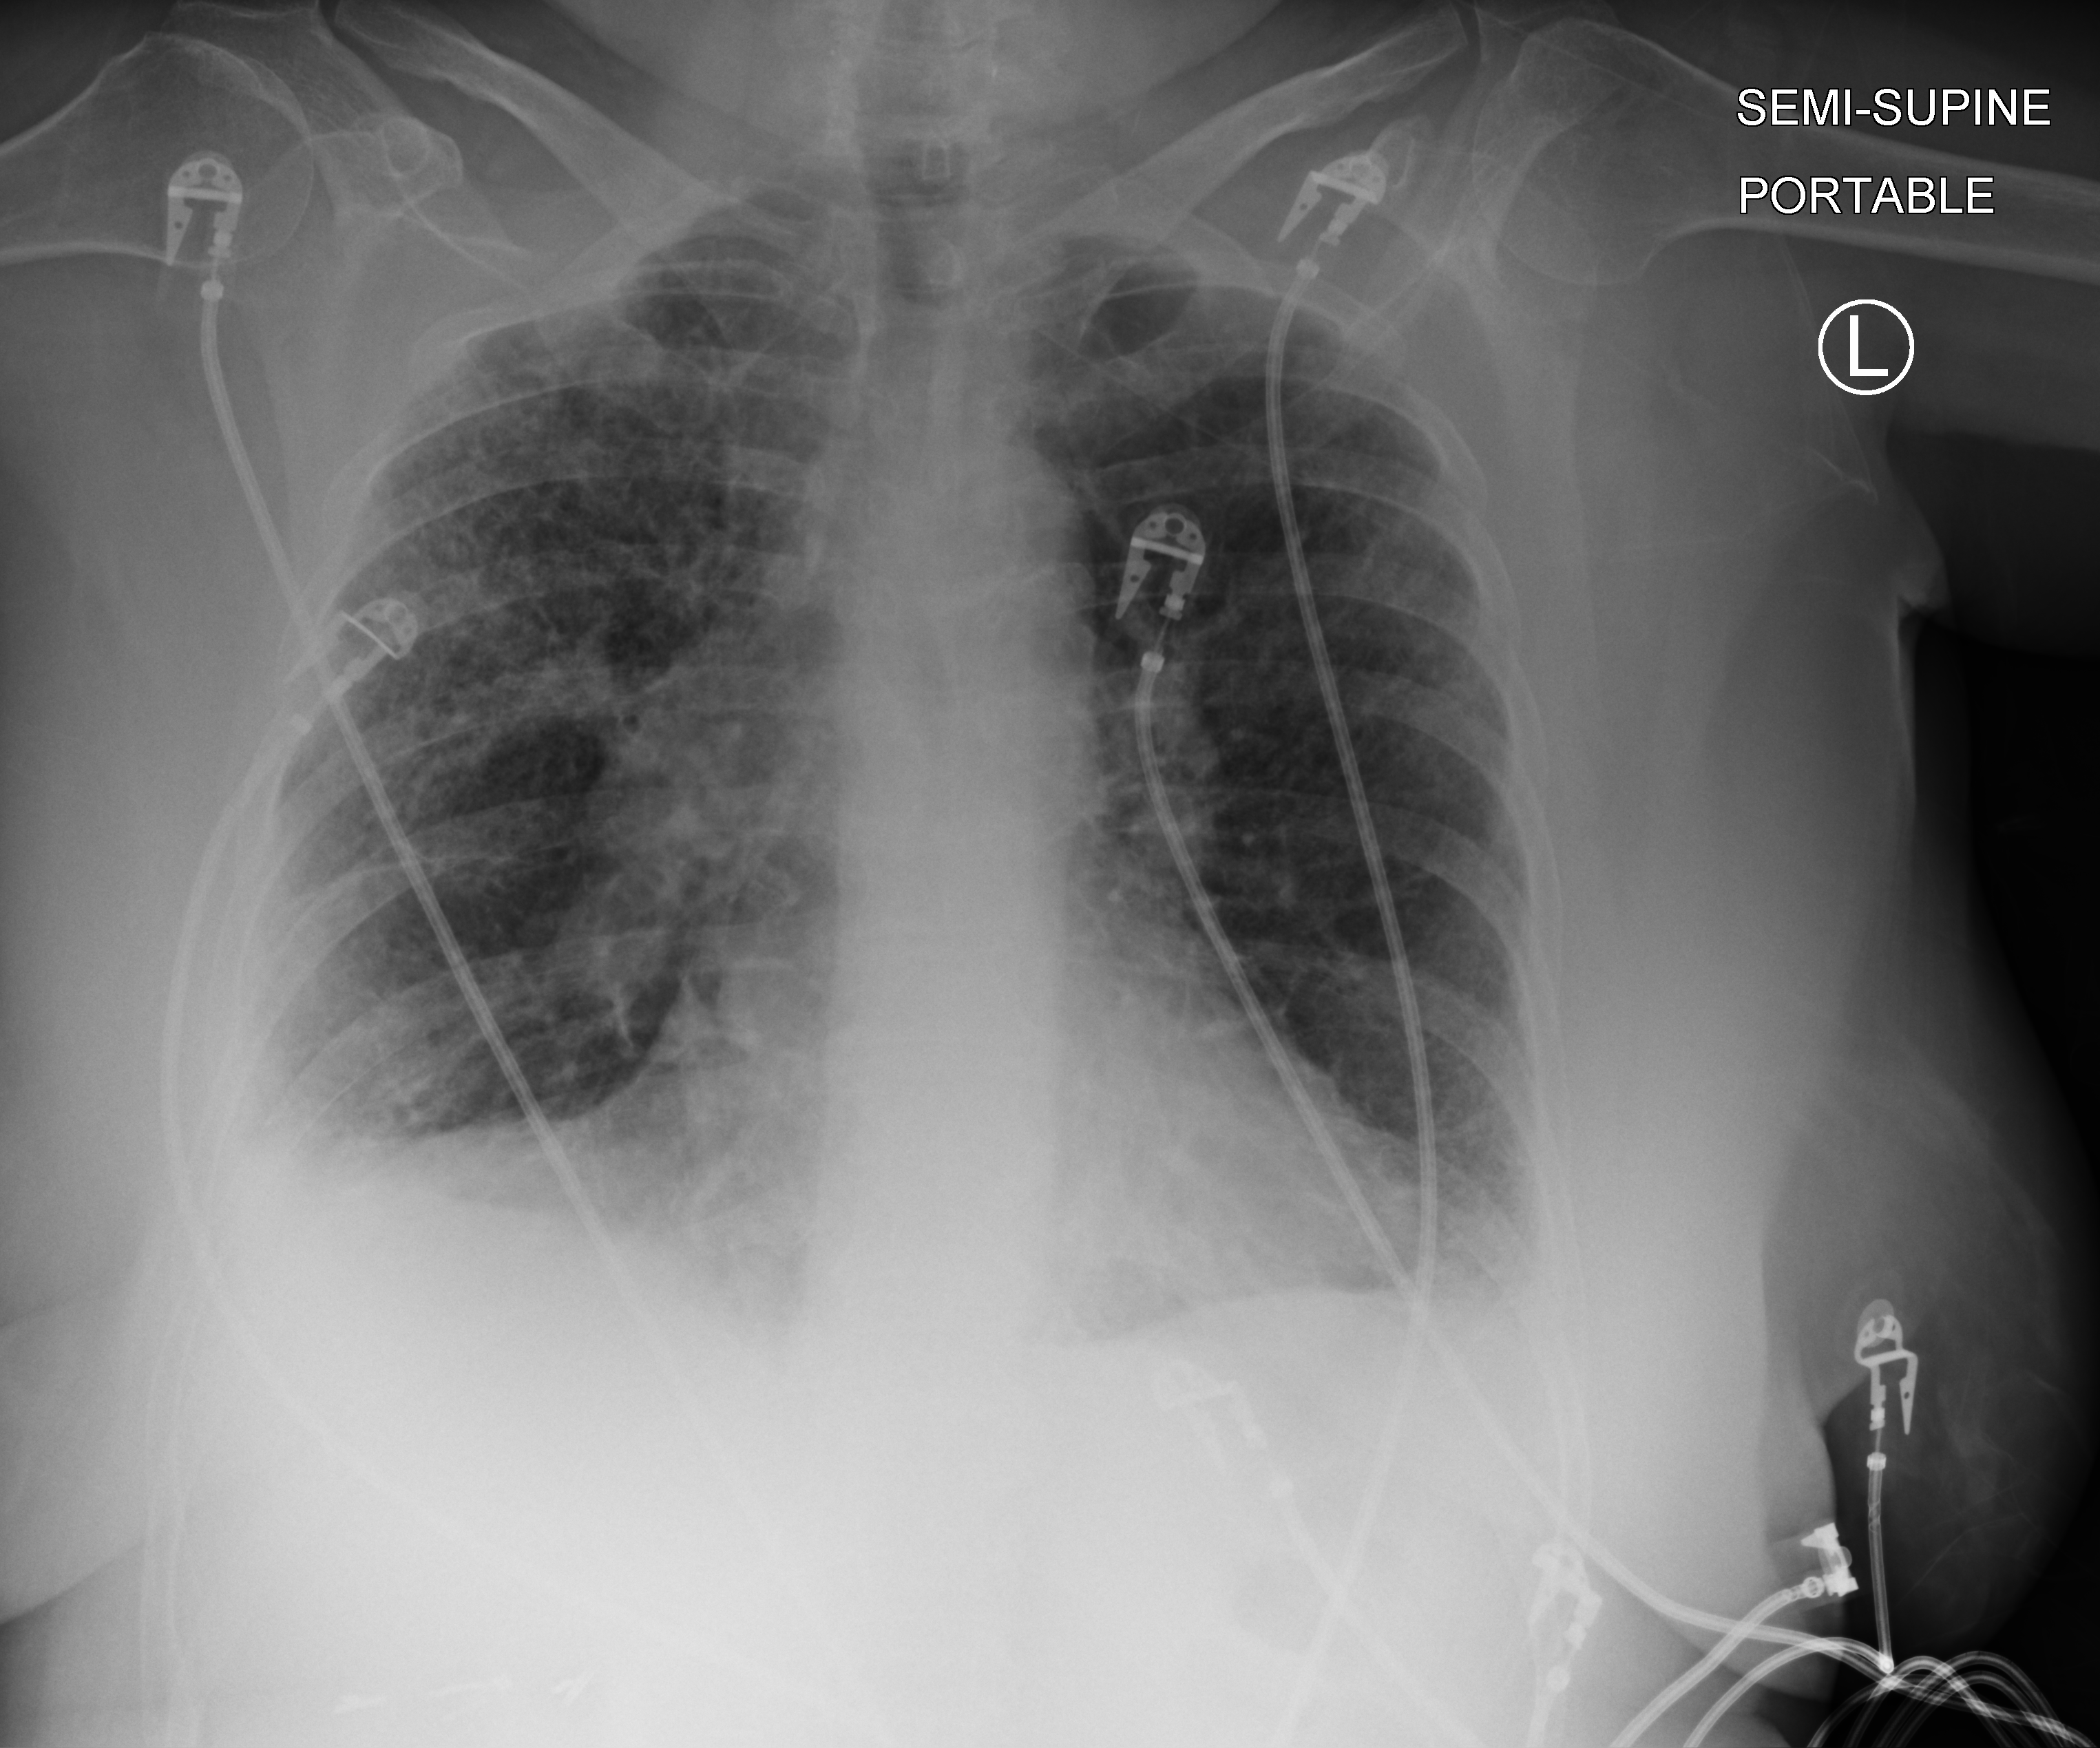
Portable chest radiograph, anteroposterior (AP) projection. Female patient hospitalised with COVID-19, age 60–74 years.
Admission-level facts for this patient (not findings on this image; timing relative to this image not recorded): diabetes (admission record): no; admitted to intensive care during this hospital stay: yes.